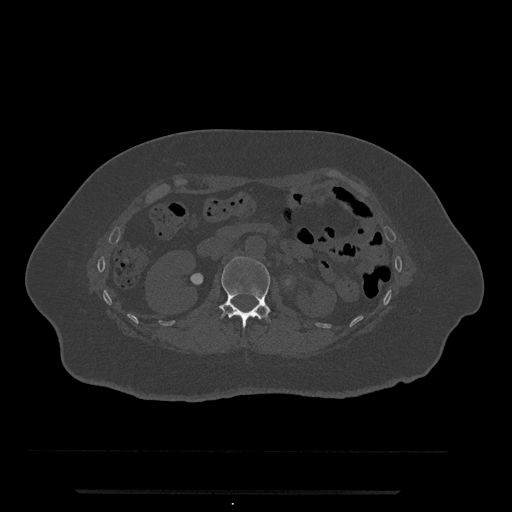
CT including the spine, one axial slice. Position 101 of 797 along the scan axis. Bone window (W 1800 / L 400 HU). 0.5 mm slice thickness. 512 × 512 image matrix. Female patient, age 51 years. From the clinical record (not read from this slice): primary cancer: neuro.
Outlined on this slice (semi-automatic segmentation, software-assisted and operator-edited):
- L1 vertebra: bounding box (x1, y1, x2, y2) in pixels: (219, 257, 271, 328)